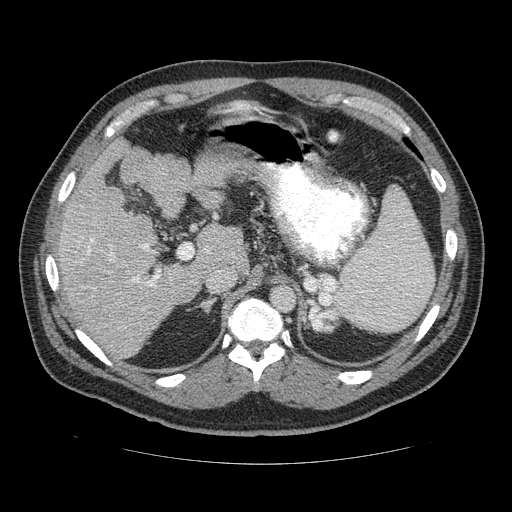
Contrast-enhanced abdominal CT (liver protocol), one axial slice. Position 84 of 113 along the scan axis. Reconstruction kernel STANDARD. 120 kVp. Soft-tissue window (W 400 / L 40 HU). 2.5 mm slice thickness. 512 × 512 image matrix. From the clinical record (not read from this slice): diagnosis: hepatocellular carcinoma (patient treated with transarterial chemoembolisation; whether this scan precedes or follows treatment is not stated here); TNM stage (as recorded): Stage-II; Child-Pugh class: B.
Outlined on this slice (semi-automatic segmentation, software-assisted and operator-edited):
- liver parenchyma outside the tumour (the mass and vessels are separate outlines, so this box may not span the whole liver): bounding box [x1, y1, x2, y2] px = [50, 104, 258, 360]
- liver vessels: [81, 214, 216, 328]